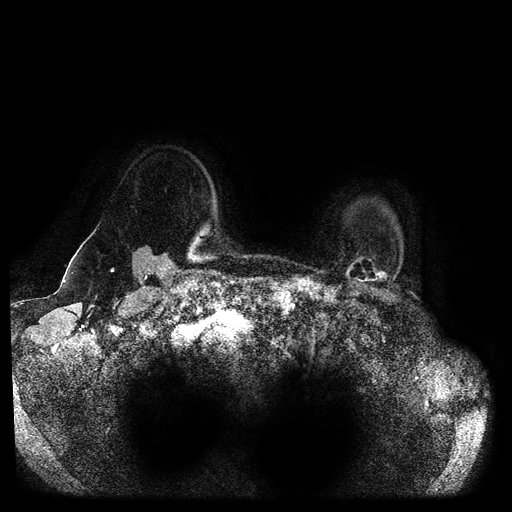
Breast MRI (dynamic contrast-enhanced, multi-phase), one axial slice. Slice 88 of 116 in the series (ordered by position). Dynamic contrast-enhanced series, time point 2 of 5 at this slice position (early post-contrast). 1.5 T. TE 2.6 ms, TR 5.3 ms. 2 mm slice thickness. 512 × 512 image matrix, field of view 370 × 370 mm. Female patient, age 55 years.
Structures marked on this image (semi-automatic segmentation, software-assisted and operator-edited):
- breast lesion (labelled benign in the annotation): bounding box <344,250,387,285> (left, top, right, bottom; pixels)